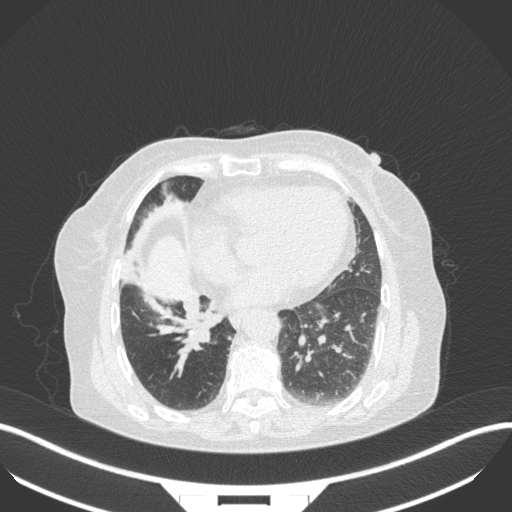
Chest CT, one axial slice; position 115 of 329 along the scan axis; 120 kVp; lung window (W 1500 / L -600 HU); 1 mm slice thickness; 512 × 512 image matrix, field of view 400 × 400 mm. Patient: female, 75 years. From the clinical record (not read from this slice): clinical TNM (as recorded): T1b N0 M1a.
Annotated regions visible in this slice (bounding box drawn by a radiologist):
- lung tumour (recorded histology: squamous cell carcinoma): box from (x=184, y=298) to (x=218, y=352) px